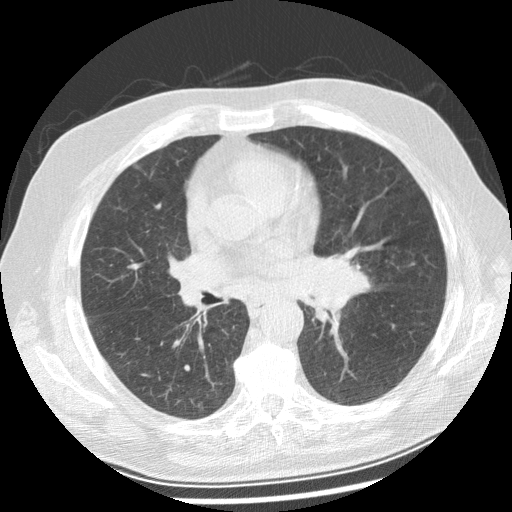
Low-dose screening chest CT, one axial slice. Position 135 of 250 along the scan axis. Lung window (W 1500 / L -600 HU). 512 × 512 image matrix, field of view 360 × 360 mm.
Outlined on this slice (manually delineated by an expert):
- lesion 1 (tumor, left main bronchus): bounding box (x1, y1, x2, y2) in pixels: (310, 266, 370, 310)